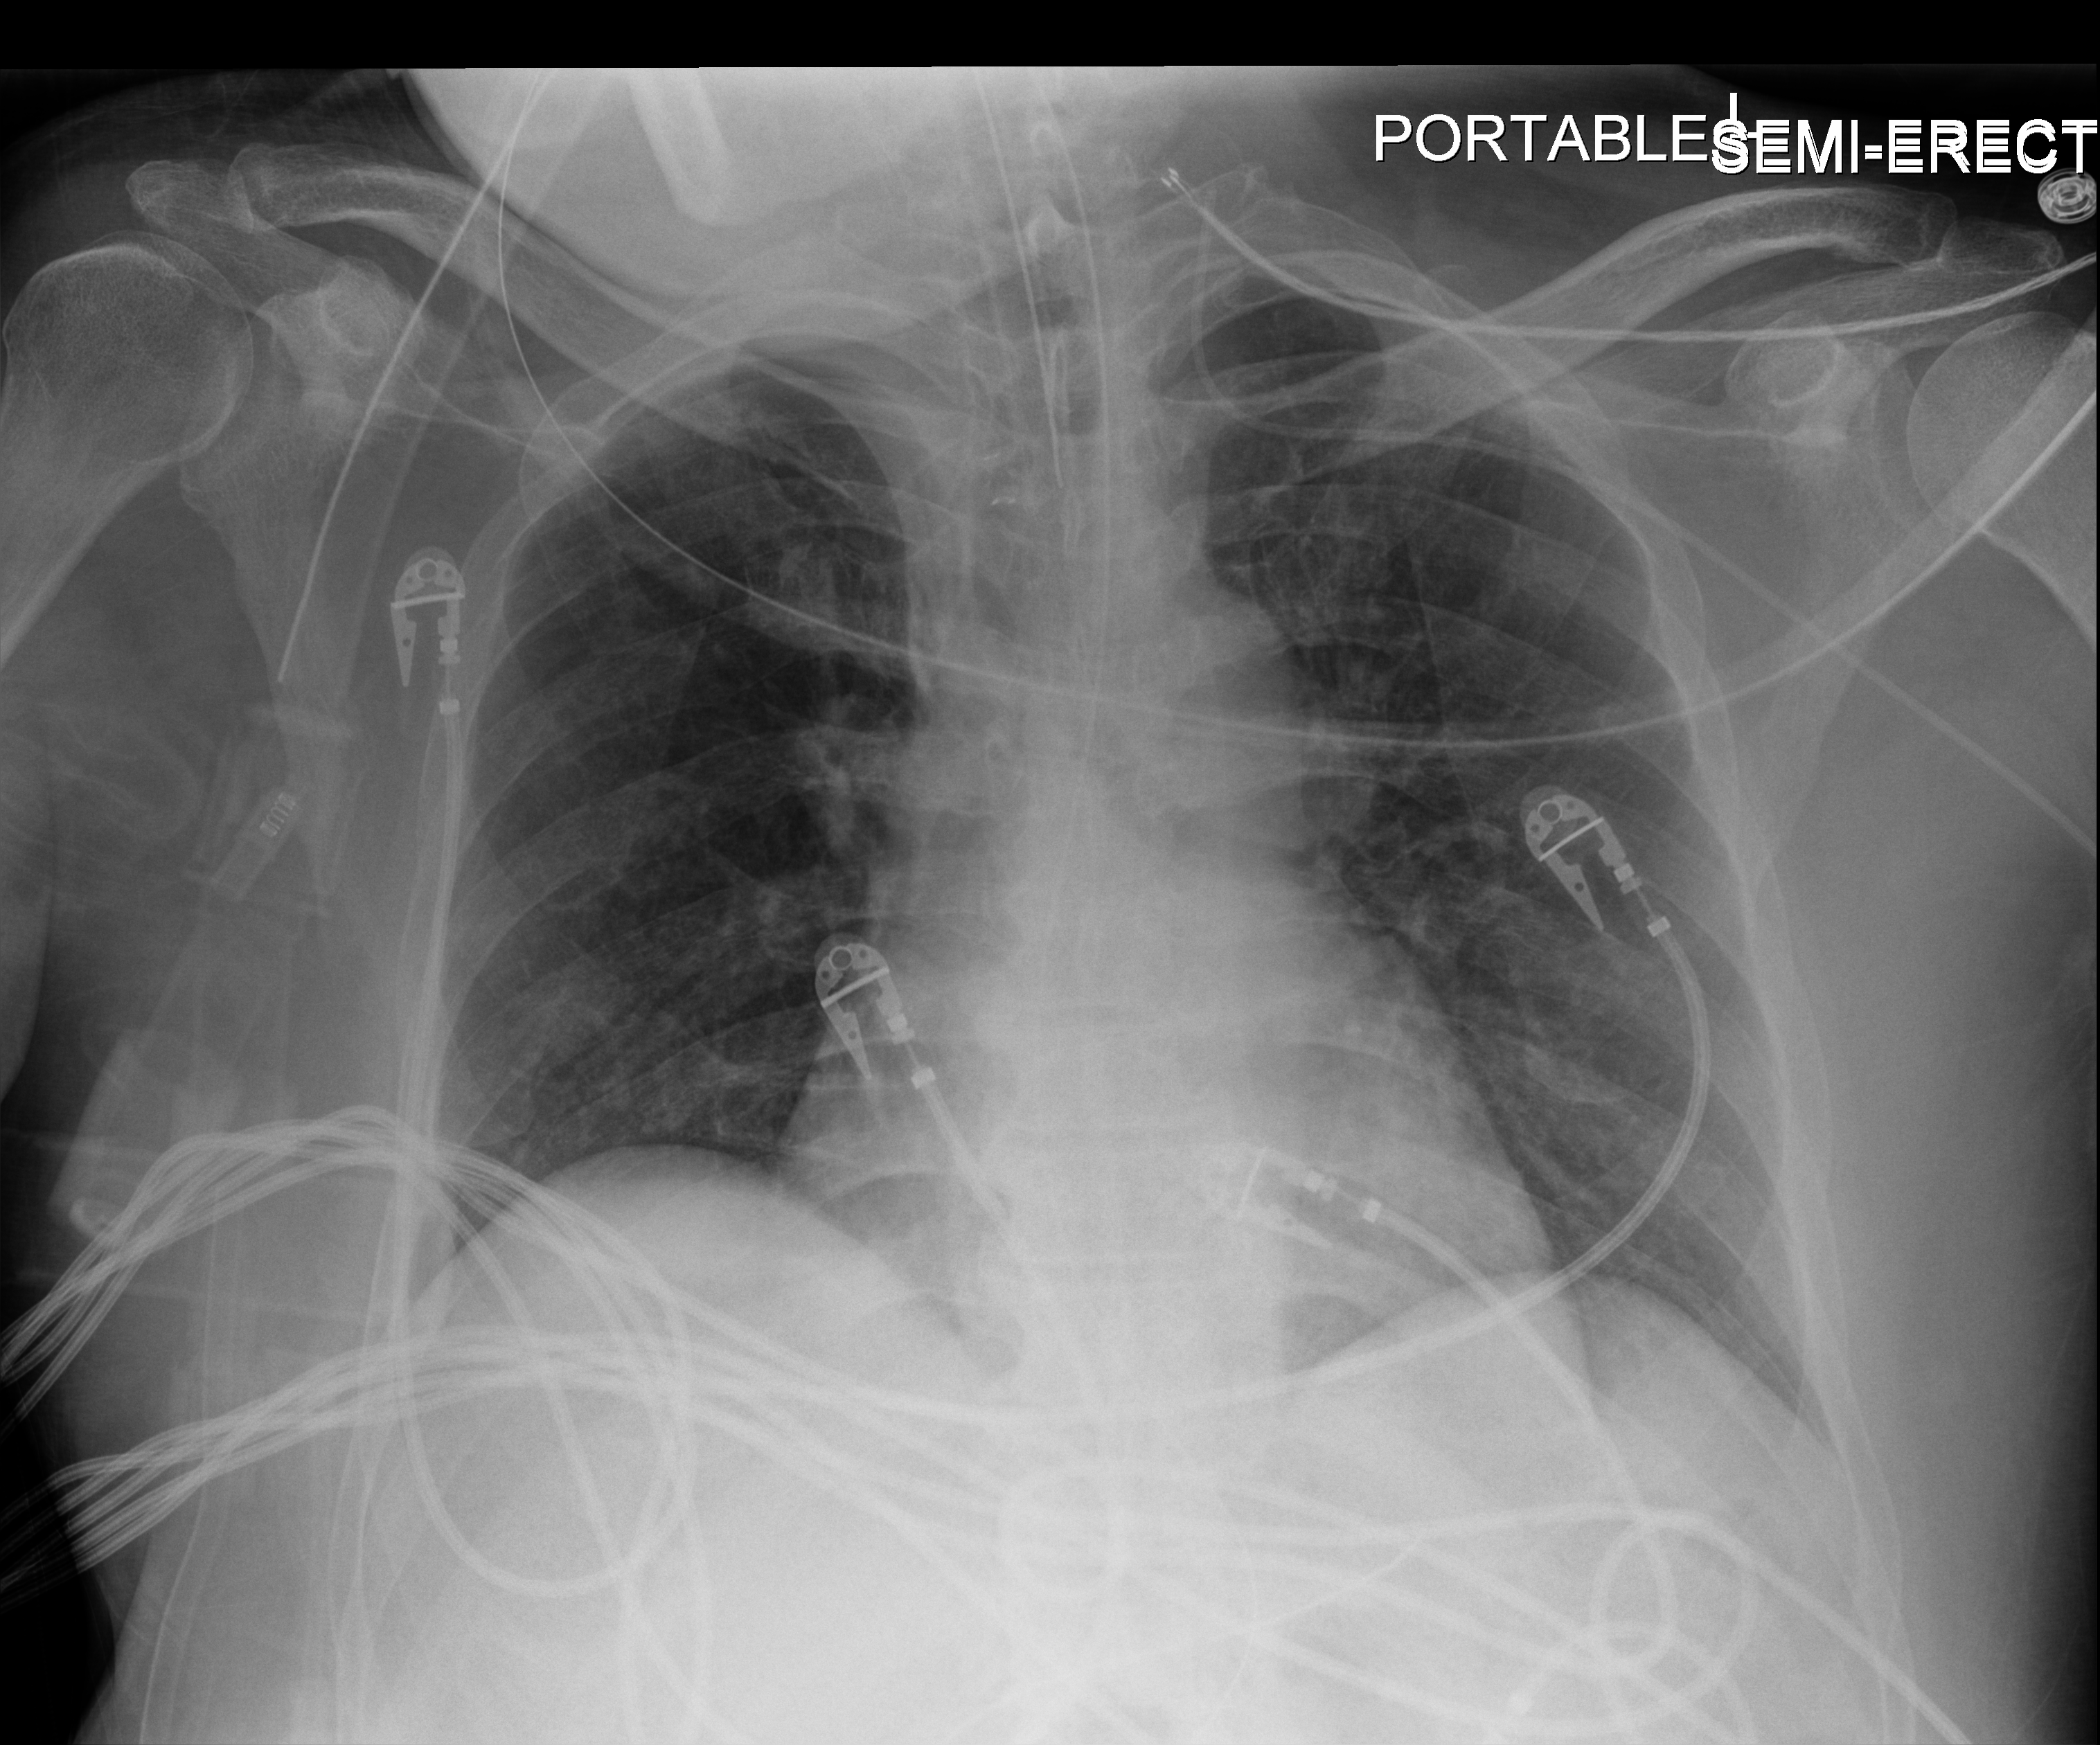
Bedside chest radiograph (digital radiography), anteroposterior (AP) projection. Patient hospitalised with COVID-19, aged 18–59 years.
Admission-level facts for this patient (not findings on this image; timing relative to this image not recorded):
- diabetes (admission record): yes